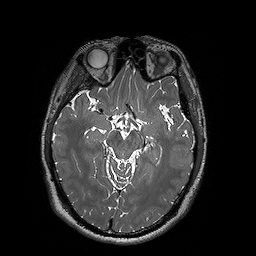
Brain MRI from a brain-tumour surgery series, one axial slice. Position 101 of 192 along the scan axis. 1 mm slice thickness. 256 × 256 image matrix, field of view 250 × 250 mm. Case-level facts recorded for this patient, not image findings: histopathology: Oligodendroglioma; WHO grade: 2; IDH mutation: yes; tumour location: Left Posterior Temporal.
Annotated regions visible in this slice (expert manual segmentation):
- tumour: bounding box [x1, y1, x2, y2] px = [159, 156, 193, 162]